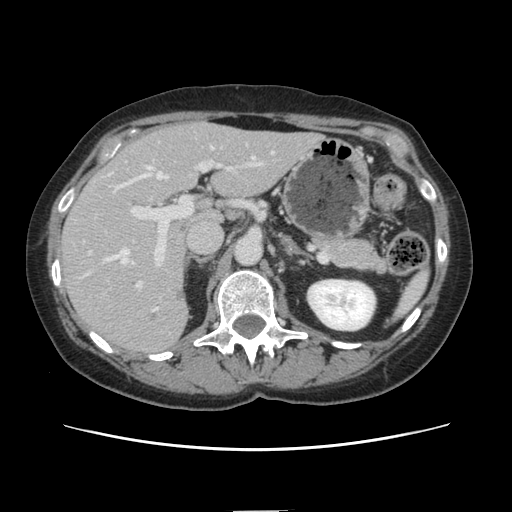
Contrast-enhanced abdominal CT, one axial slice; position 80 of 141 along the scan axis; 120 kVp; intravenous contrast given; soft-tissue window (W 400 / L 40 HU); 2.5 mm slice thickness; 512 × 512 image matrix, field of view 350 × 350 mm. Female patient, age 63 years. From the clinical record (not read from this slice): diagnosis: colorectal cancer liver metastases, imaged before liver resection; multiple liver metastases: yes; largest metastasis: 3.2 cm.
Annotated regions visible in this slice (expert manual segmentation):
- hepatic veins: box from (x=82, y=157) to (x=260, y=278) px
- liver: (x=60, y=123)–(x=318, y=354)
- planned liver remnant (the part of the liver to remain after resection): (x=175, y=123)–(x=318, y=222)
- portal vein (with intrahepatic branches): (x=131, y=159)–(x=255, y=292)
- liver metastasis: (x=173, y=290)–(x=186, y=304)
- liver metastasis: (x=147, y=312)–(x=160, y=324)